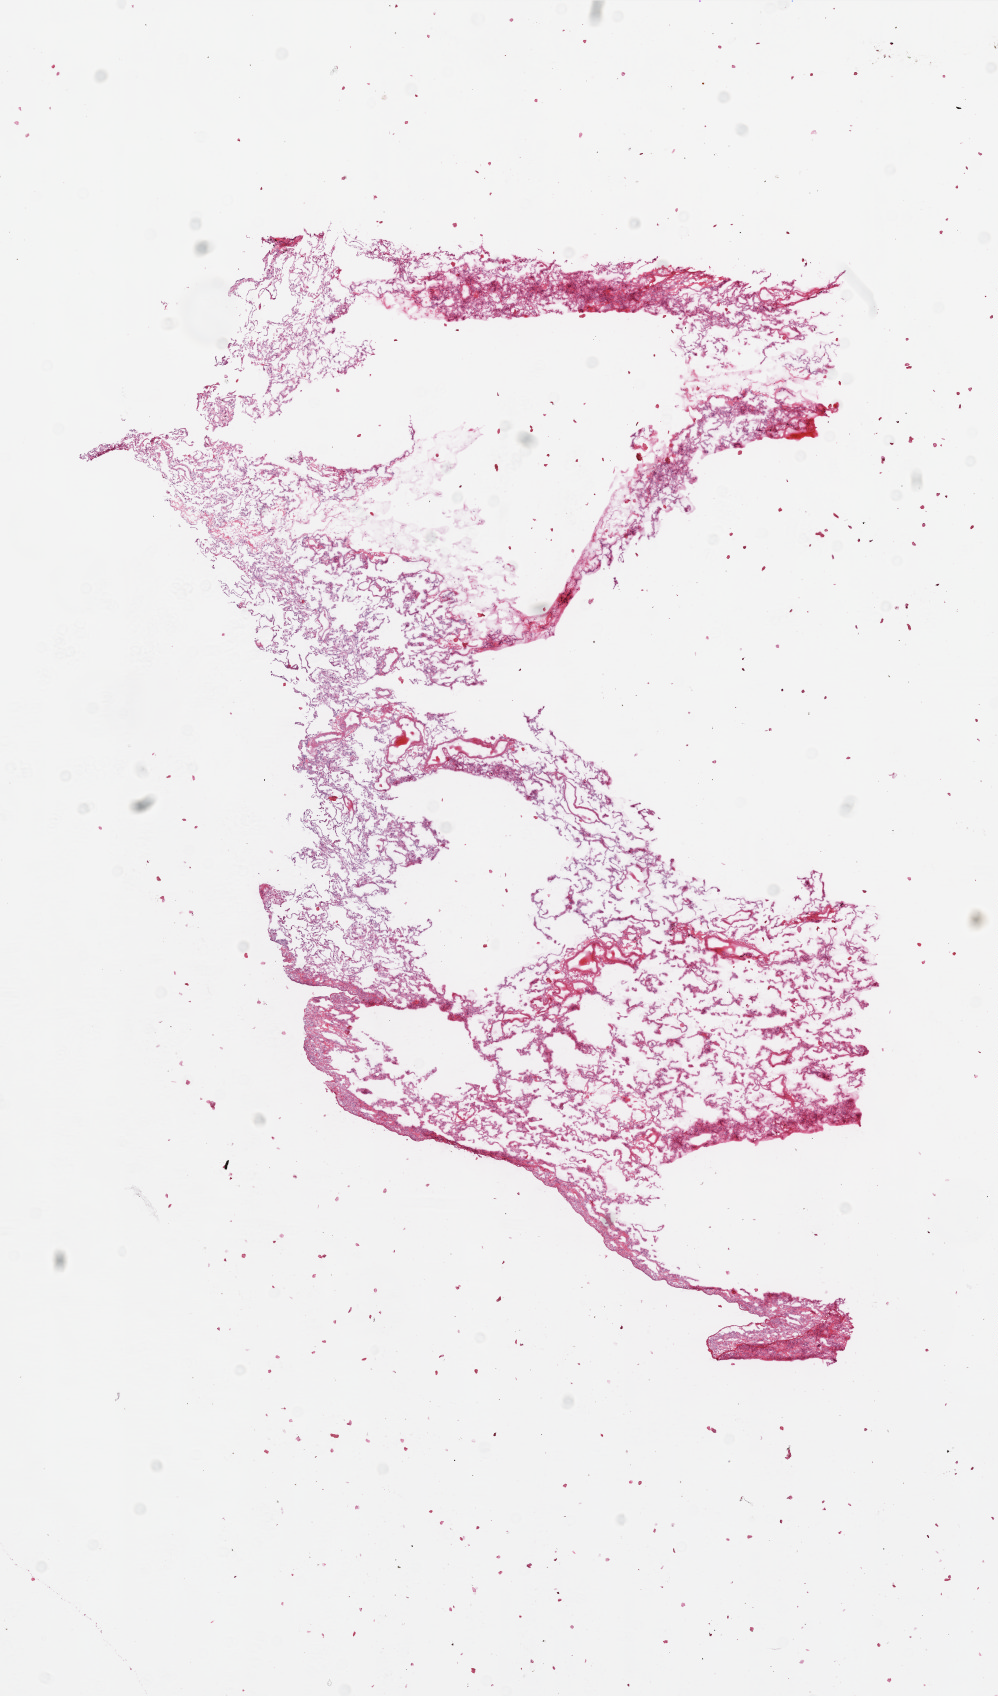
H&E-stained whole-slide image, a low-resolution overview of the entire scanned area, about 8.0 x 13.6 mm (from a 20x scan). Frozen section. Solid tissue normal (non-tumour tissue) sample from the lung. Patient: male, age at initial diagnosis 71 years.
This section: solid tissue normal sample (biorepository sample class). Patient diagnosis: Squamous cell carcinoma, NOS.